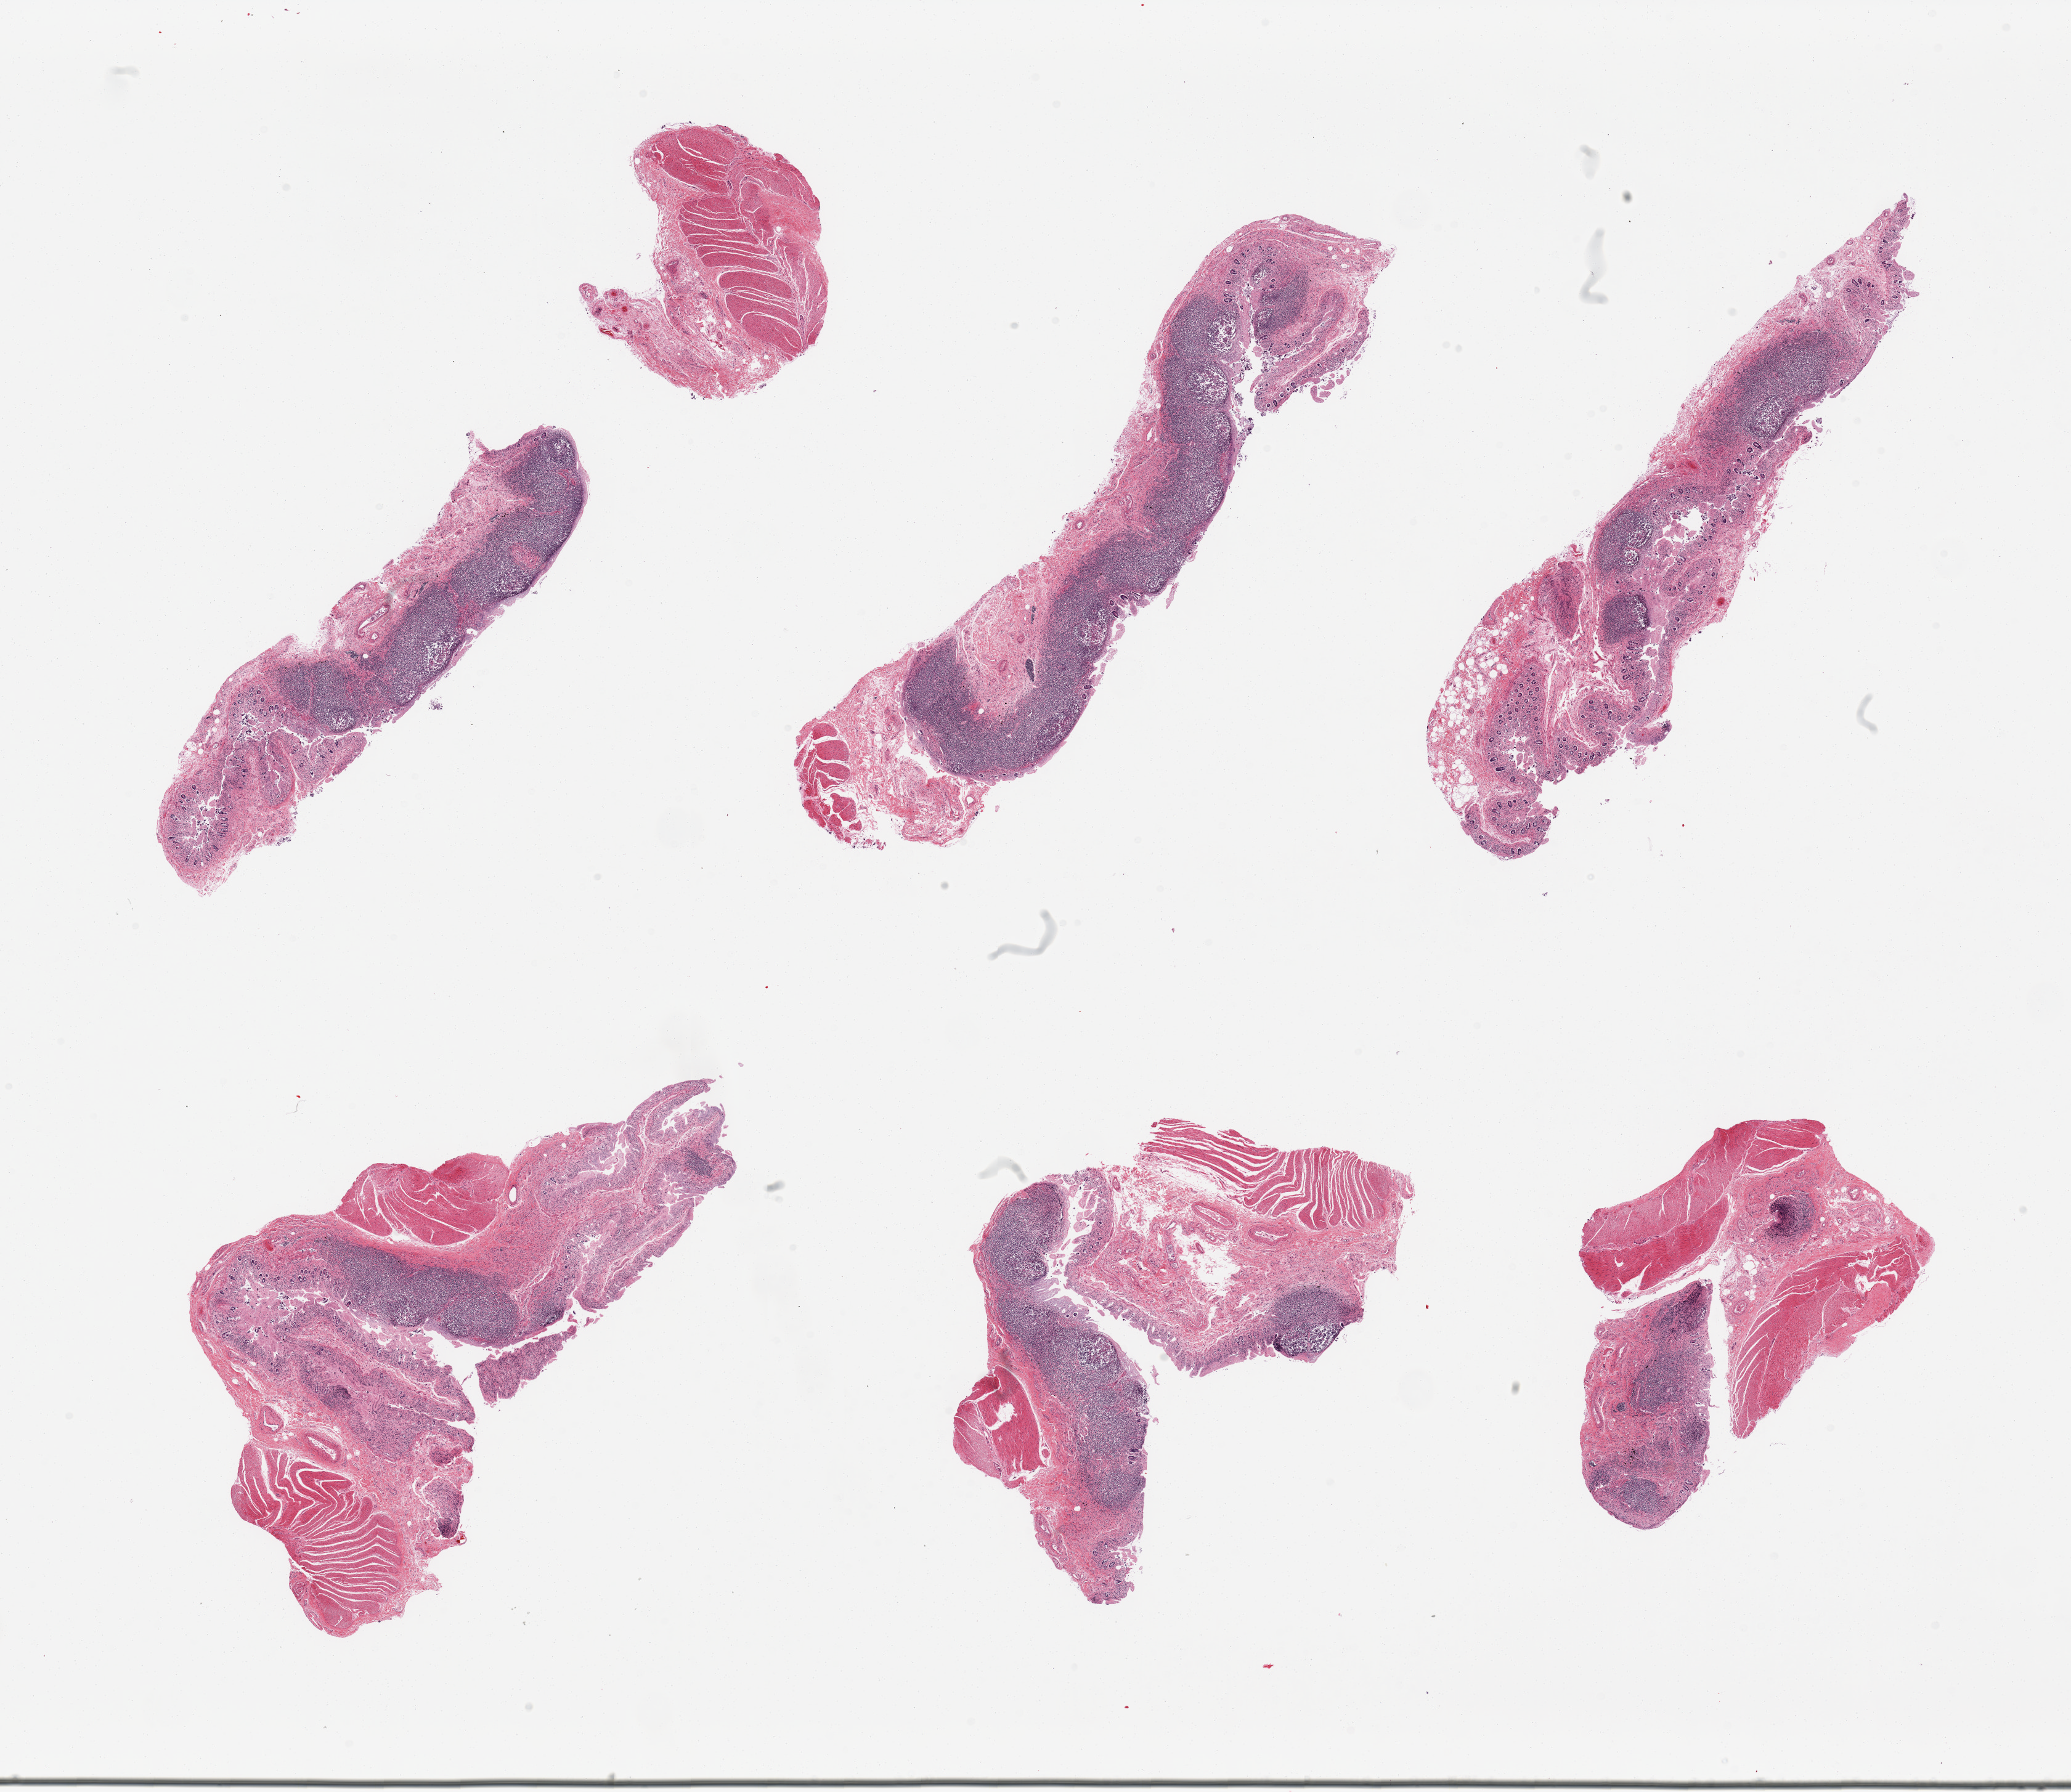
Digitized H&E-stained section — a low-resolution overview of the entire scanned area, about 26.6 x 23.0 mm; PAXgene-fixed, paraffin-embedded tissue; target tissue: ileum; donor tissue sample. Male donor.
Reviewer comment on this tissue sample: 7 pieces, severely autolyzed mucosa with good lymphoid component, includes some muscularis (not target).